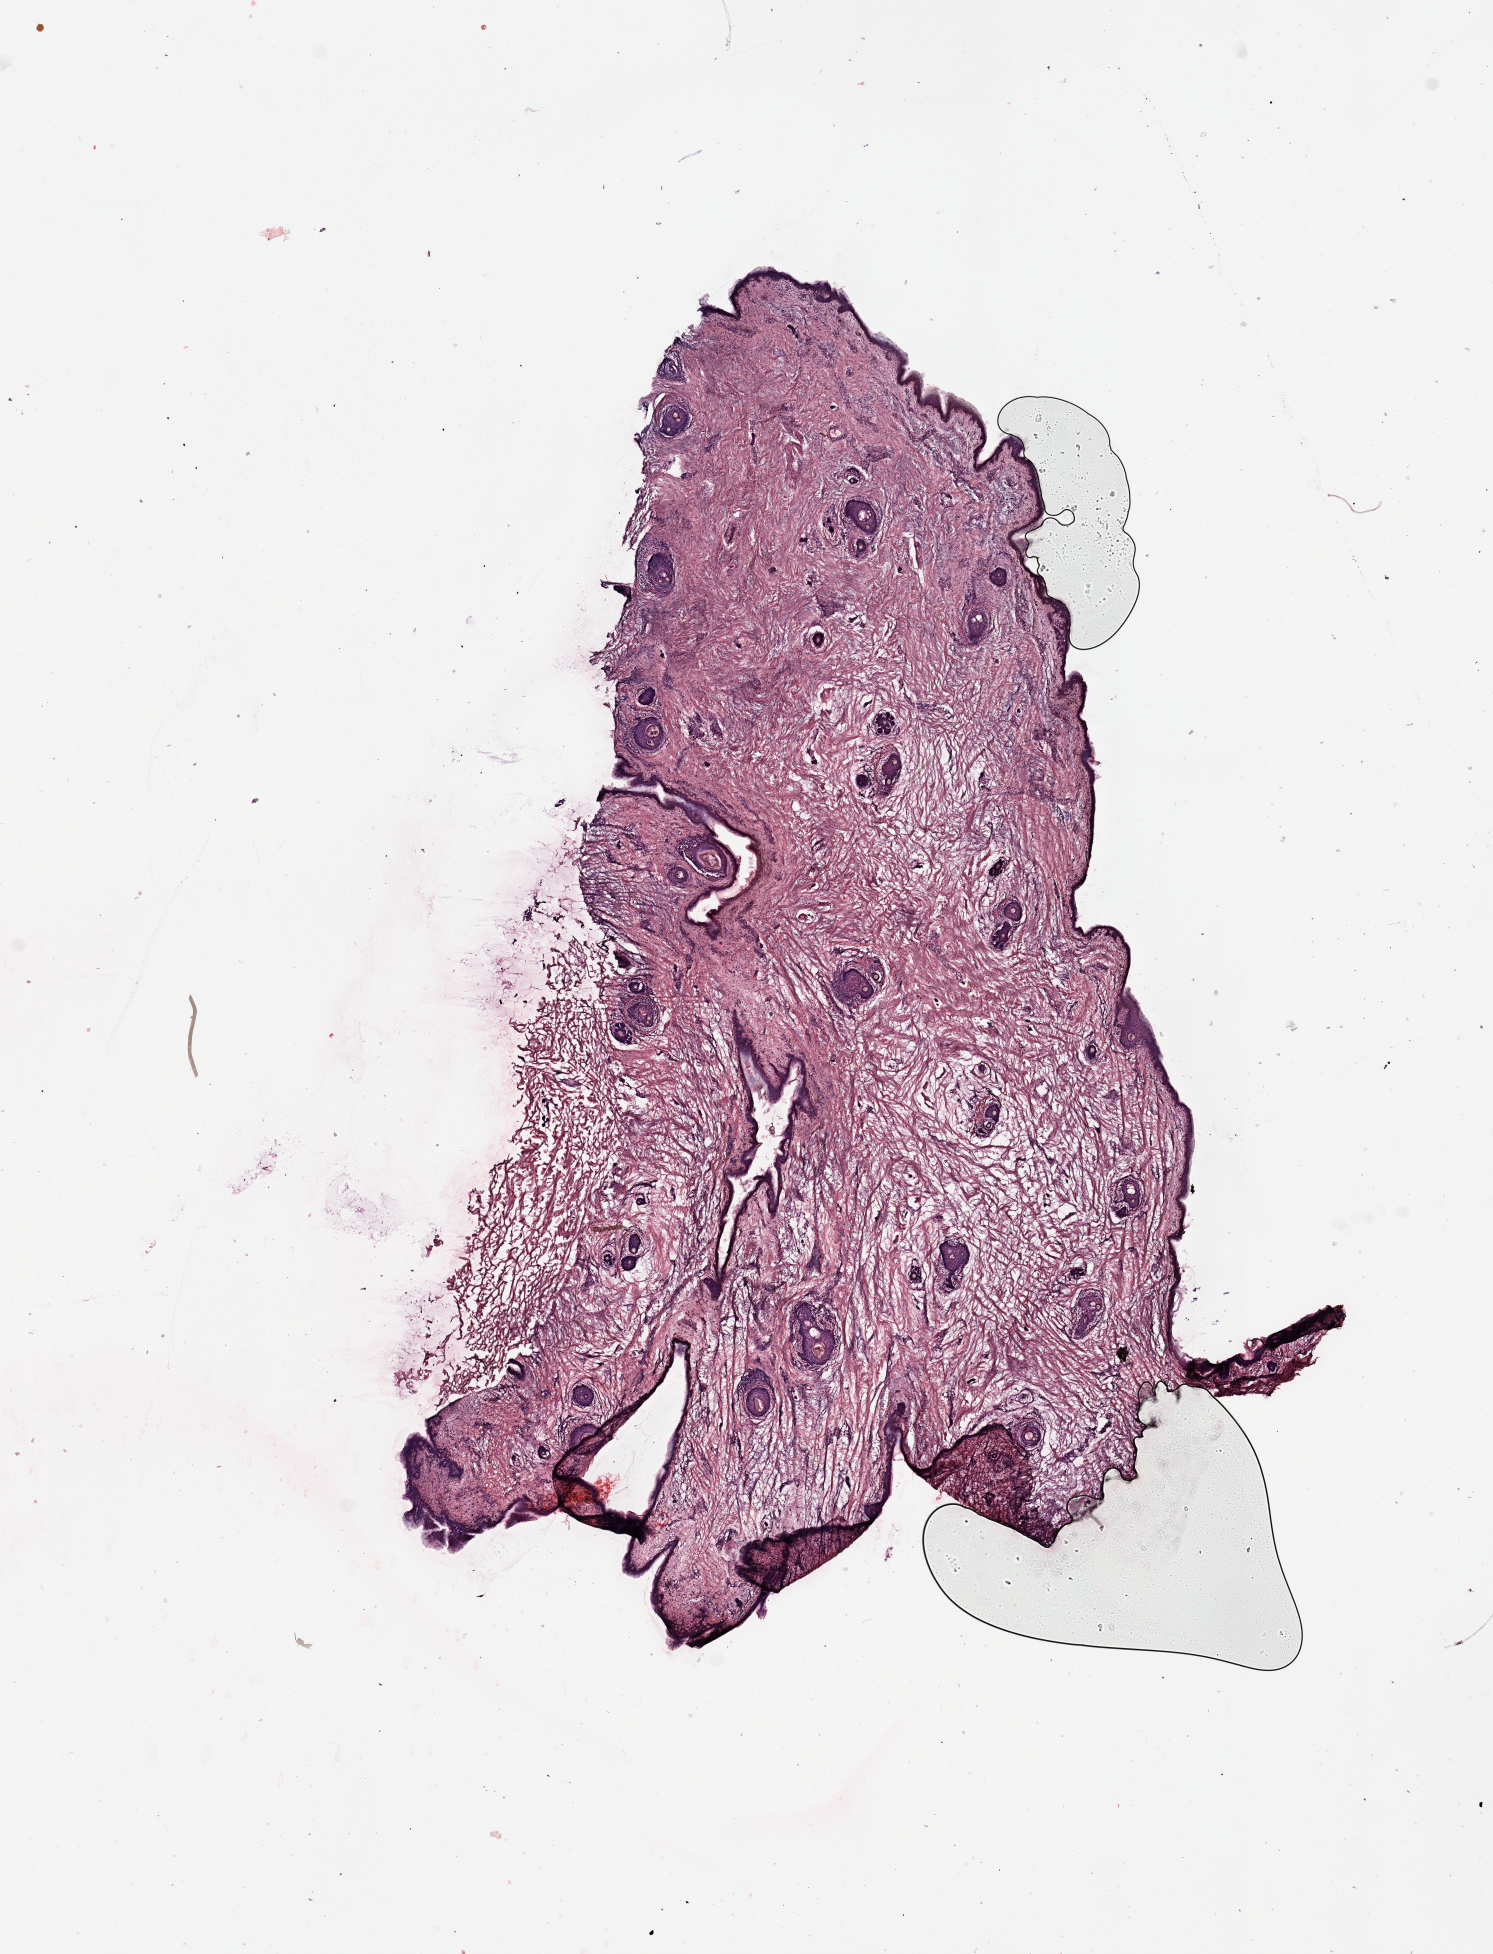
Whole-slide histology image, Hematoxylin and eosin (H&E) stained, shown as a low-resolution overview of the whole scanned area (about 11.8 x 15.5 mm, slide scanned at 20x), normal (non-tumour) tissue (melanoma cohort); sampled site not recorded. Patient: female, age 53 years.
This section: normal (non-tumour) tissue from the same patient. Patient diagnosis (cohort enrolment): cutaneous melanoma (skin).